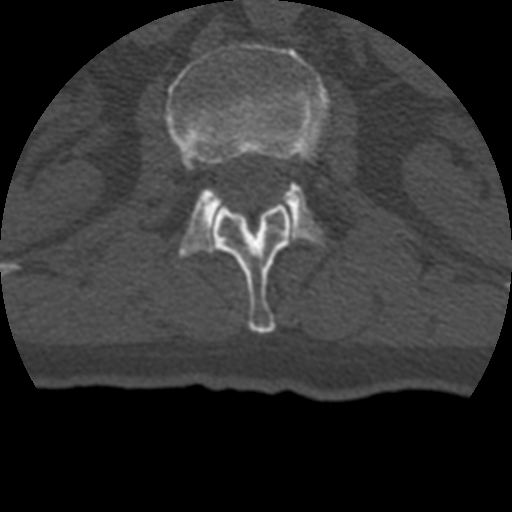
CT including the spine, one axial slice. Position 132 of 399 along the scan axis. Reconstruction kernel STANDARD. Bone window (W 1800 / L 400 HU). 1.25 mm slice thickness. 512 × 512 image matrix, field of view 160 × 160 mm. Patient age 69 years. Case-level facts recorded for this patient, not image findings: primary cancer: prostate.
Outlined on this slice (semi-automatic segmentation, software-assisted and operator-edited):
- L1 vertebra: bounding box [x1, y1, x2, y2] px = [212, 204, 294, 334]
- L2 vertebra: [165, 44, 329, 257]